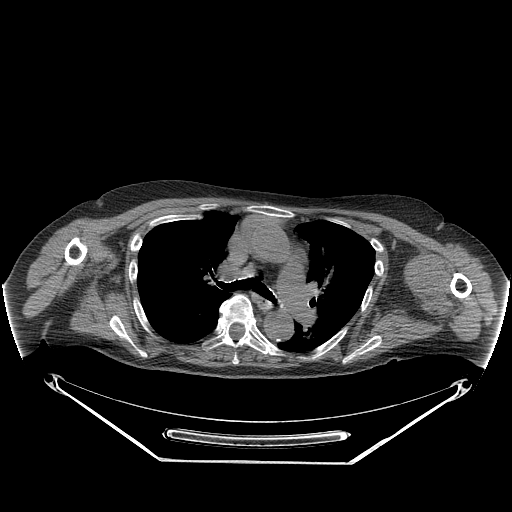
CT of an extremity soft-tissue mass (from a PET/CT study), one axial slice. Position 184 of 267 along the scan axis. 140 kVp. Soft-tissue window (W 400 / L 40 HU). 3.75 mm slice thickness. 512 × 512 image matrix, field of view 500 × 500 mm. Female patient. From the clinical record (not read from this slice): histological type: pleiomorphic leiomyosarcoma; grade: high; site of the primary tumour: left biceps.
Annotated regions visible in this slice (expert contour drawn on MRI and transferred to this co-registered scan by the dataset authors):
- gross tumour volume including surrounding oedema: bounding box (x1, y1, x2, y2) in pixels: (411, 253, 444, 305)
- gross tumour volume (mass): (411, 256, 442, 291)